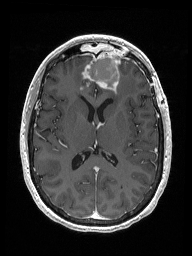
Brain MRI from a brain-tumour surgery series, one axial slice. Slice 79 of 192 in the series (ordered by position). T1-weighted post-contrast. 1 mm slice thickness. 192 × 256 image matrix. From the clinical record (not read from this slice): histopathology: Metastastic Carcinoma from Breast primary.
Outlined on this slice (expert manual segmentation):
- previous resection cavity: bounding box <85,52,119,87> (left, top, right, bottom; pixels)